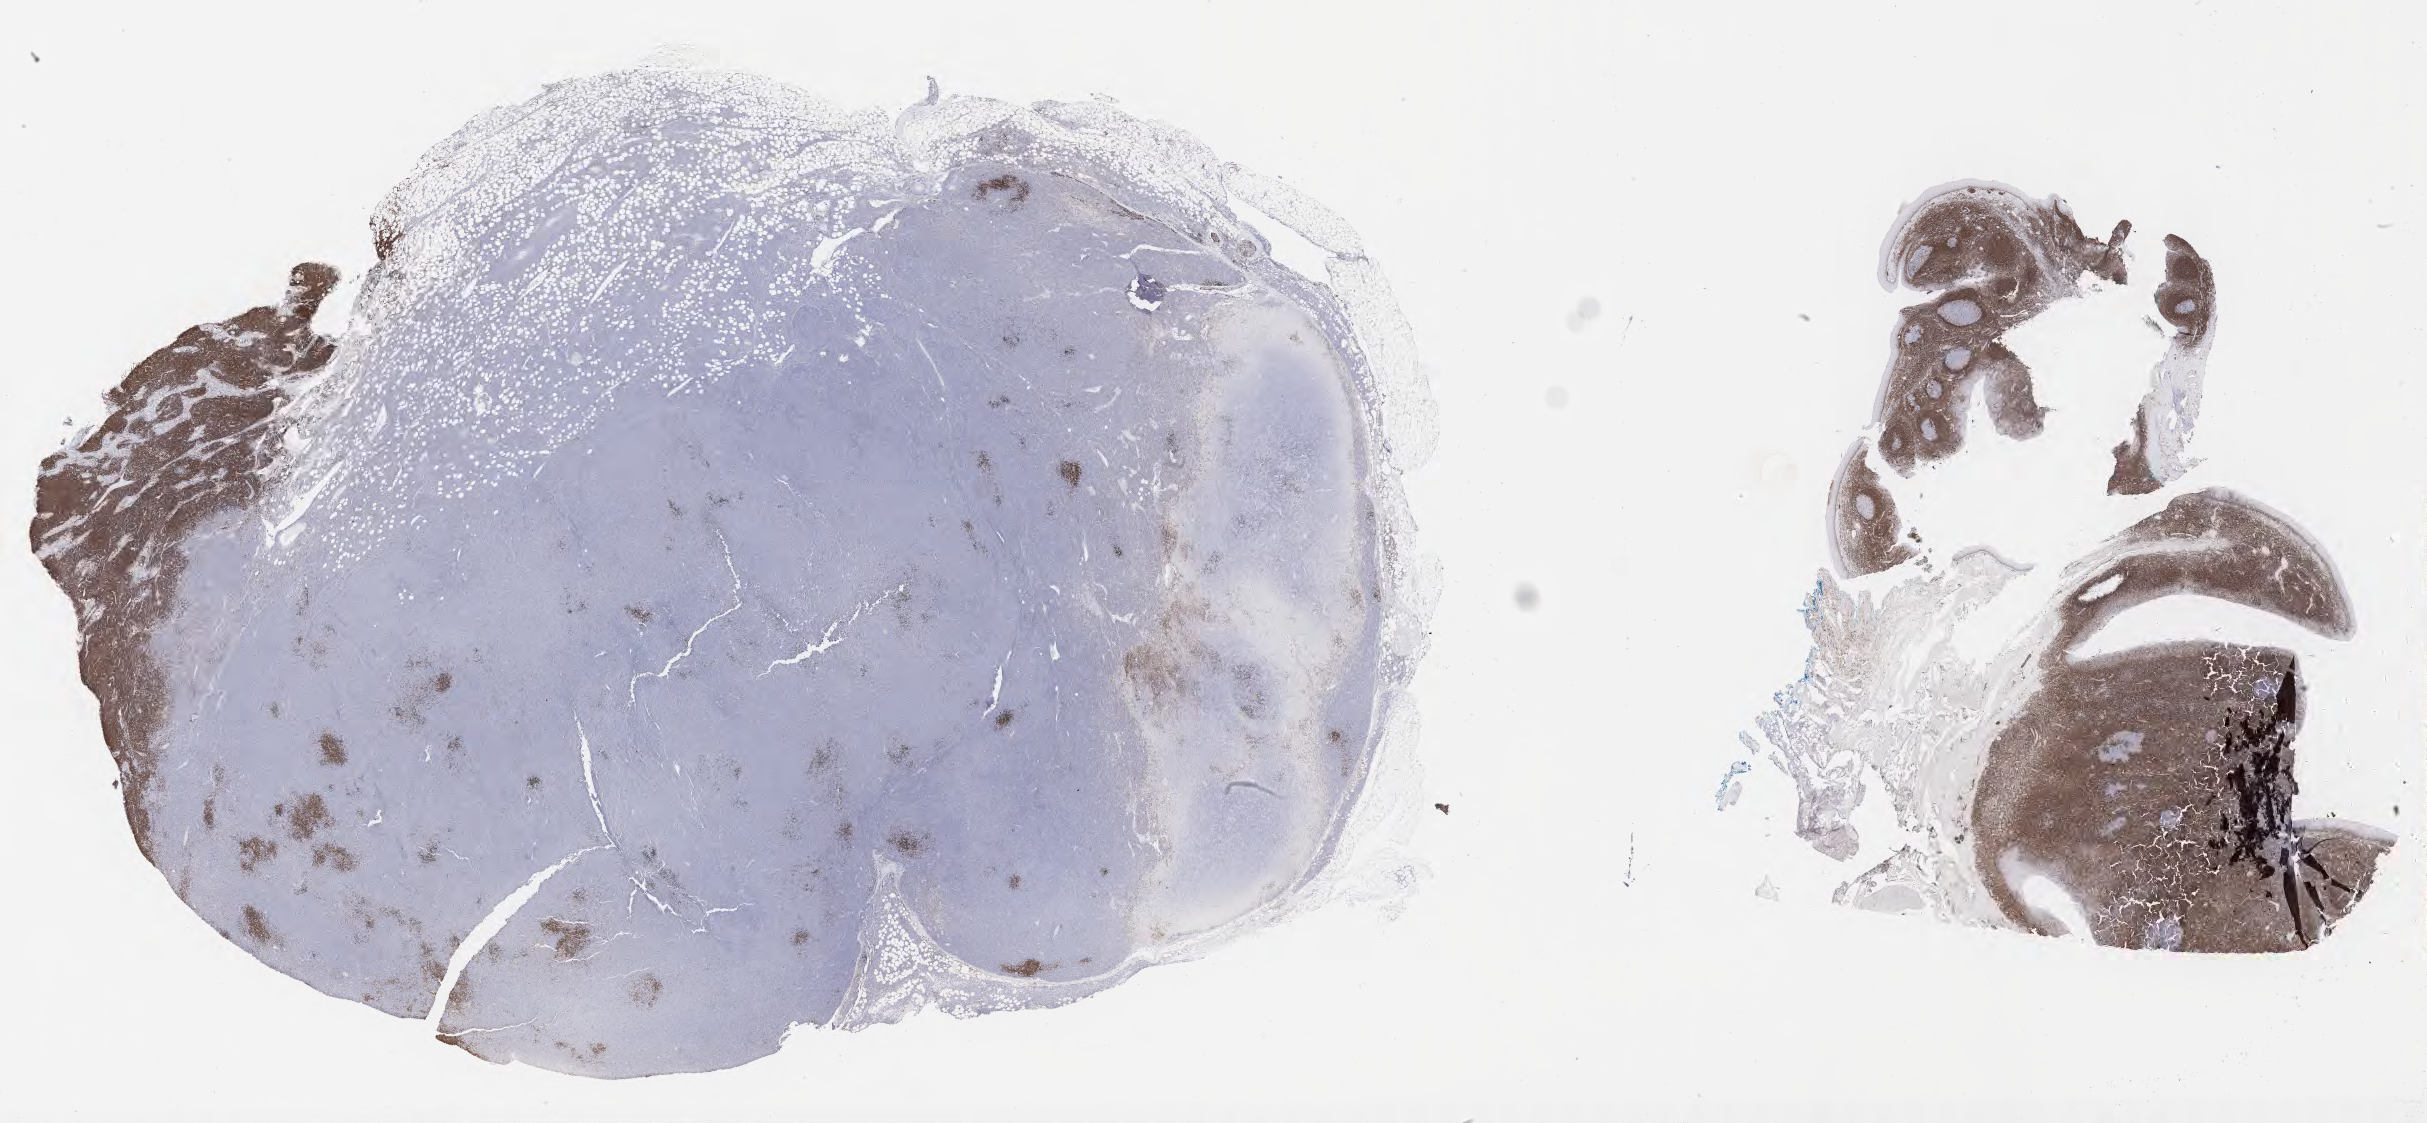
Whole-slide image, immunohistochemical stain for BCL2 — shown as a low-resolution overview of the whole scanned area (about 39.2 x 18.2 mm); tumor tissue. Patient: male, aged 57.
Histologic diagnosis: Burkitt lymphoma, NOS.